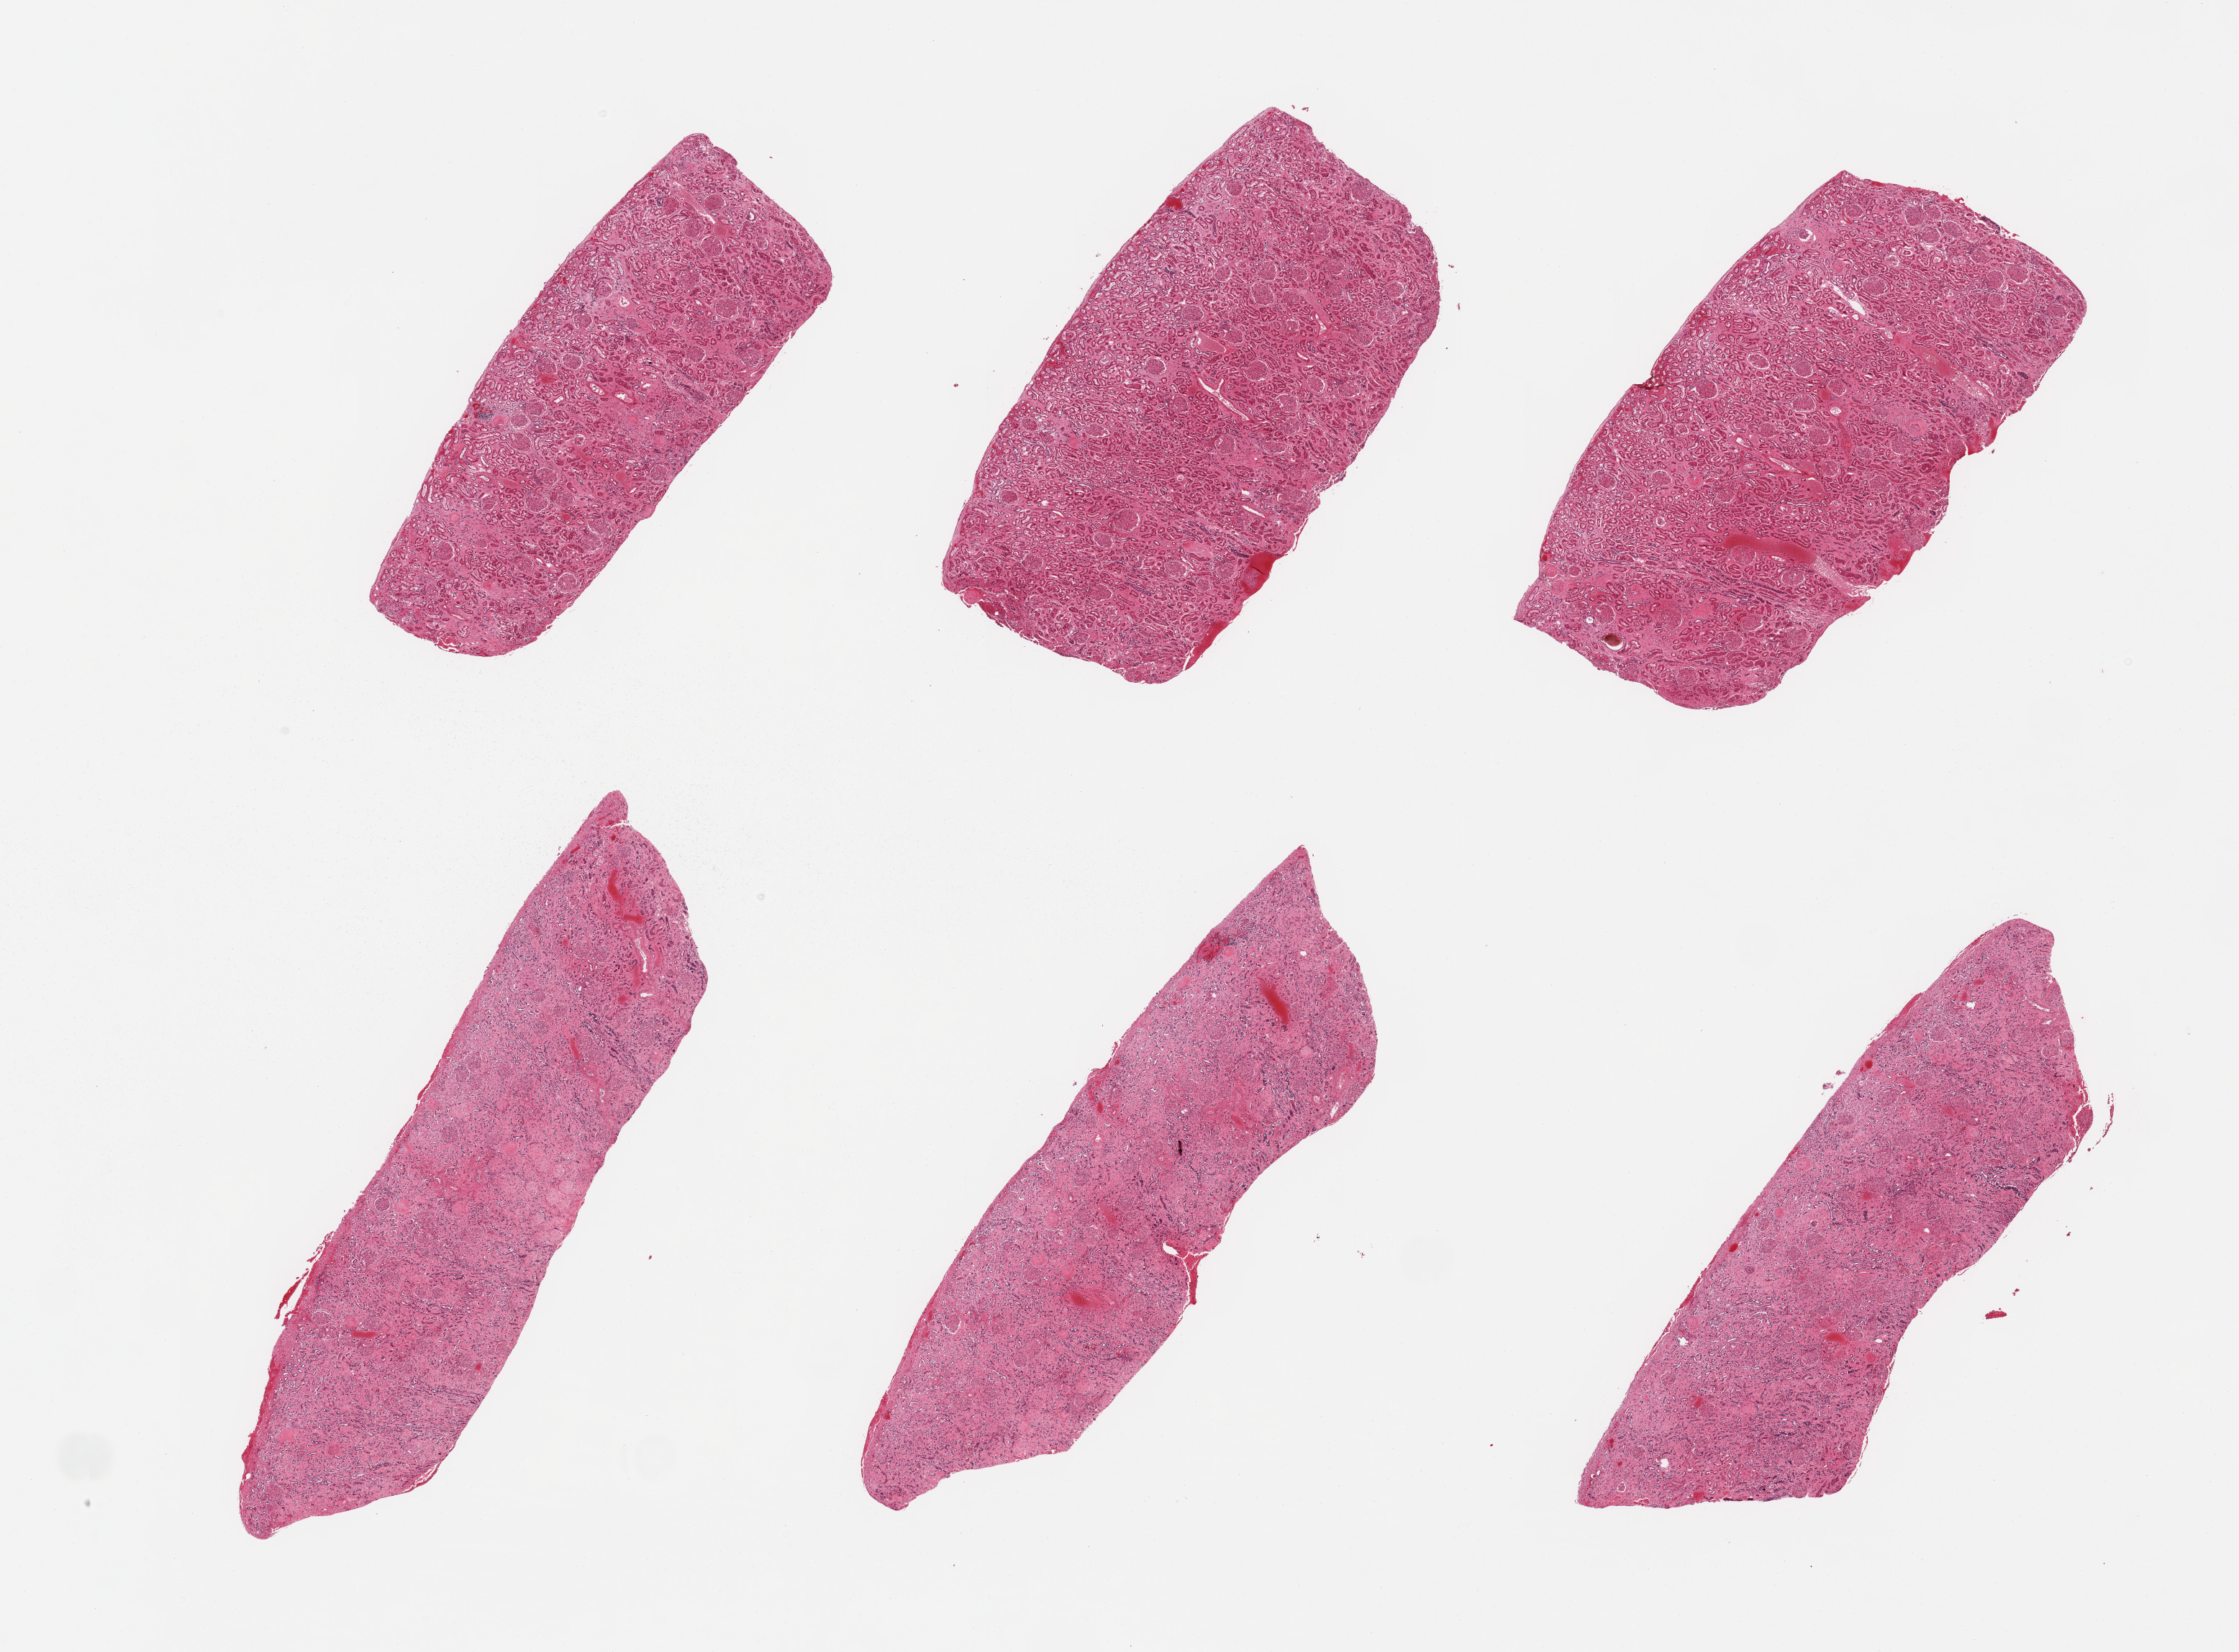
Hematoxylin and eosin (H&E) whole-slide image, brightfield, whole scanned area (about 24.6 x 18.2 mm, from a 20x scan) shown as a low-resolution overview; PAXgene-fixed, paraffin-embedded tissue; target tissue: renal cortex; donor tissue sample. Donor: male.
Reviewer comment on this tissue sample: 6 pieces, glomeruli present, interstitial fibrosis, tubules autolyzing.